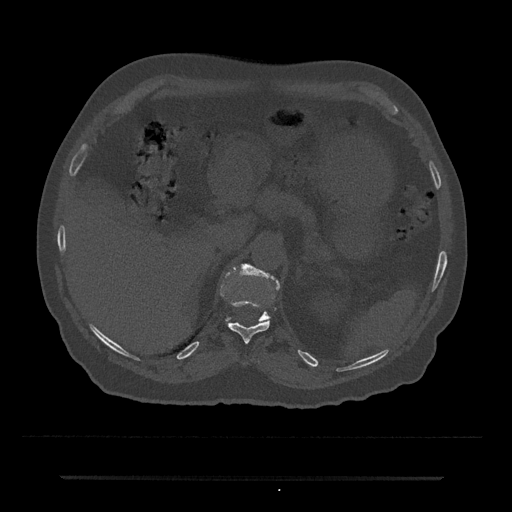
CT including the spine, one axial slice. Reconstruction kernel Br40s/3. Bone window (W 1800 / L 400 HU). 512 × 512 image matrix. Patient: male, 69 years. From the clinical record (not read from this slice): primary cancer: prostate.
Annotated regions visible in this slice (semi-automatic segmentation, software-assisted and operator-edited):
- T11 vertebra: bounding box (x1, y1, x2, y2) in pixels: (227, 300, 270, 343)
- T12 vertebra: (226, 264, 280, 322)